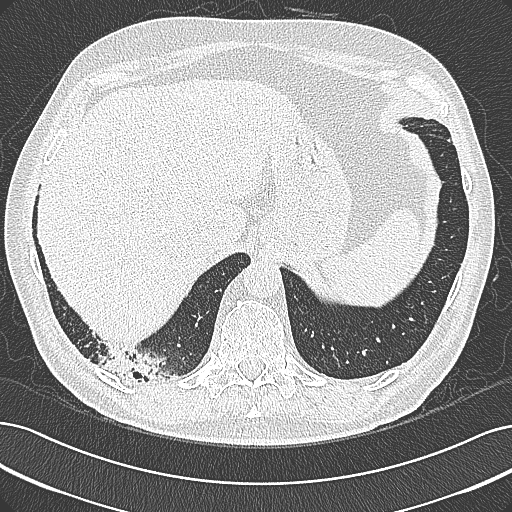
Axial slice from a low-dose chest CT screening exam, baseline annual screen, lung window (W 1500 / L -600 HU), slice 255 of 355 in the series. Male participant, aged 68 years at enrolment.
- Expert-annotated lung lesion, bounding box <94,337,194,397> (left, top, right, bottom; pixels).
- No non-calcified nodule or mass ≥4 mm was recorded by the screening reader at this exam.
- Official screen result: negative screen, significant abnormalities not suspicious for lung cancer.
- Later outcome: lung cancer diagnosed 154 days after this screen — mucinous adenocarcinoma, right lower lobe, well differentiated (G1), stage IB (AJCC 6th edition), 50 mm at pathology.